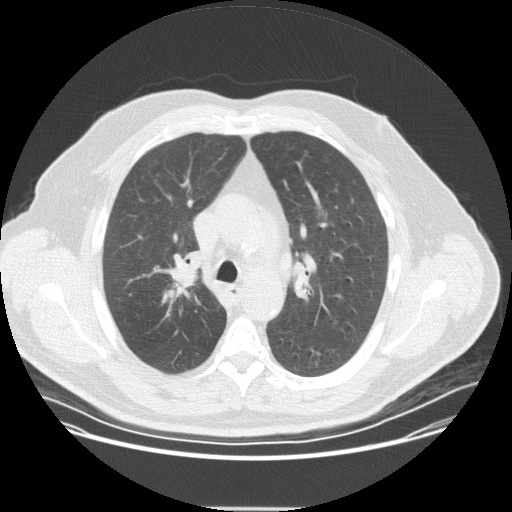
Low-dose screening chest CT, one axial slice. Slice 235 of 351 in the series (ordered by position). Reconstruction kernel STANDARD. 120 kVp. Lung window (W 1500 / L -600 HU). 2.5 mm slice thickness. 512 × 512 image matrix, field of view 419 × 419 mm.
Outlined on this slice (manually delineated by an expert):
- lesion 1 (tumor, upper lobe of right lung): bounding box (x1, y1, x2, y2) in pixels: (163, 266, 199, 303)